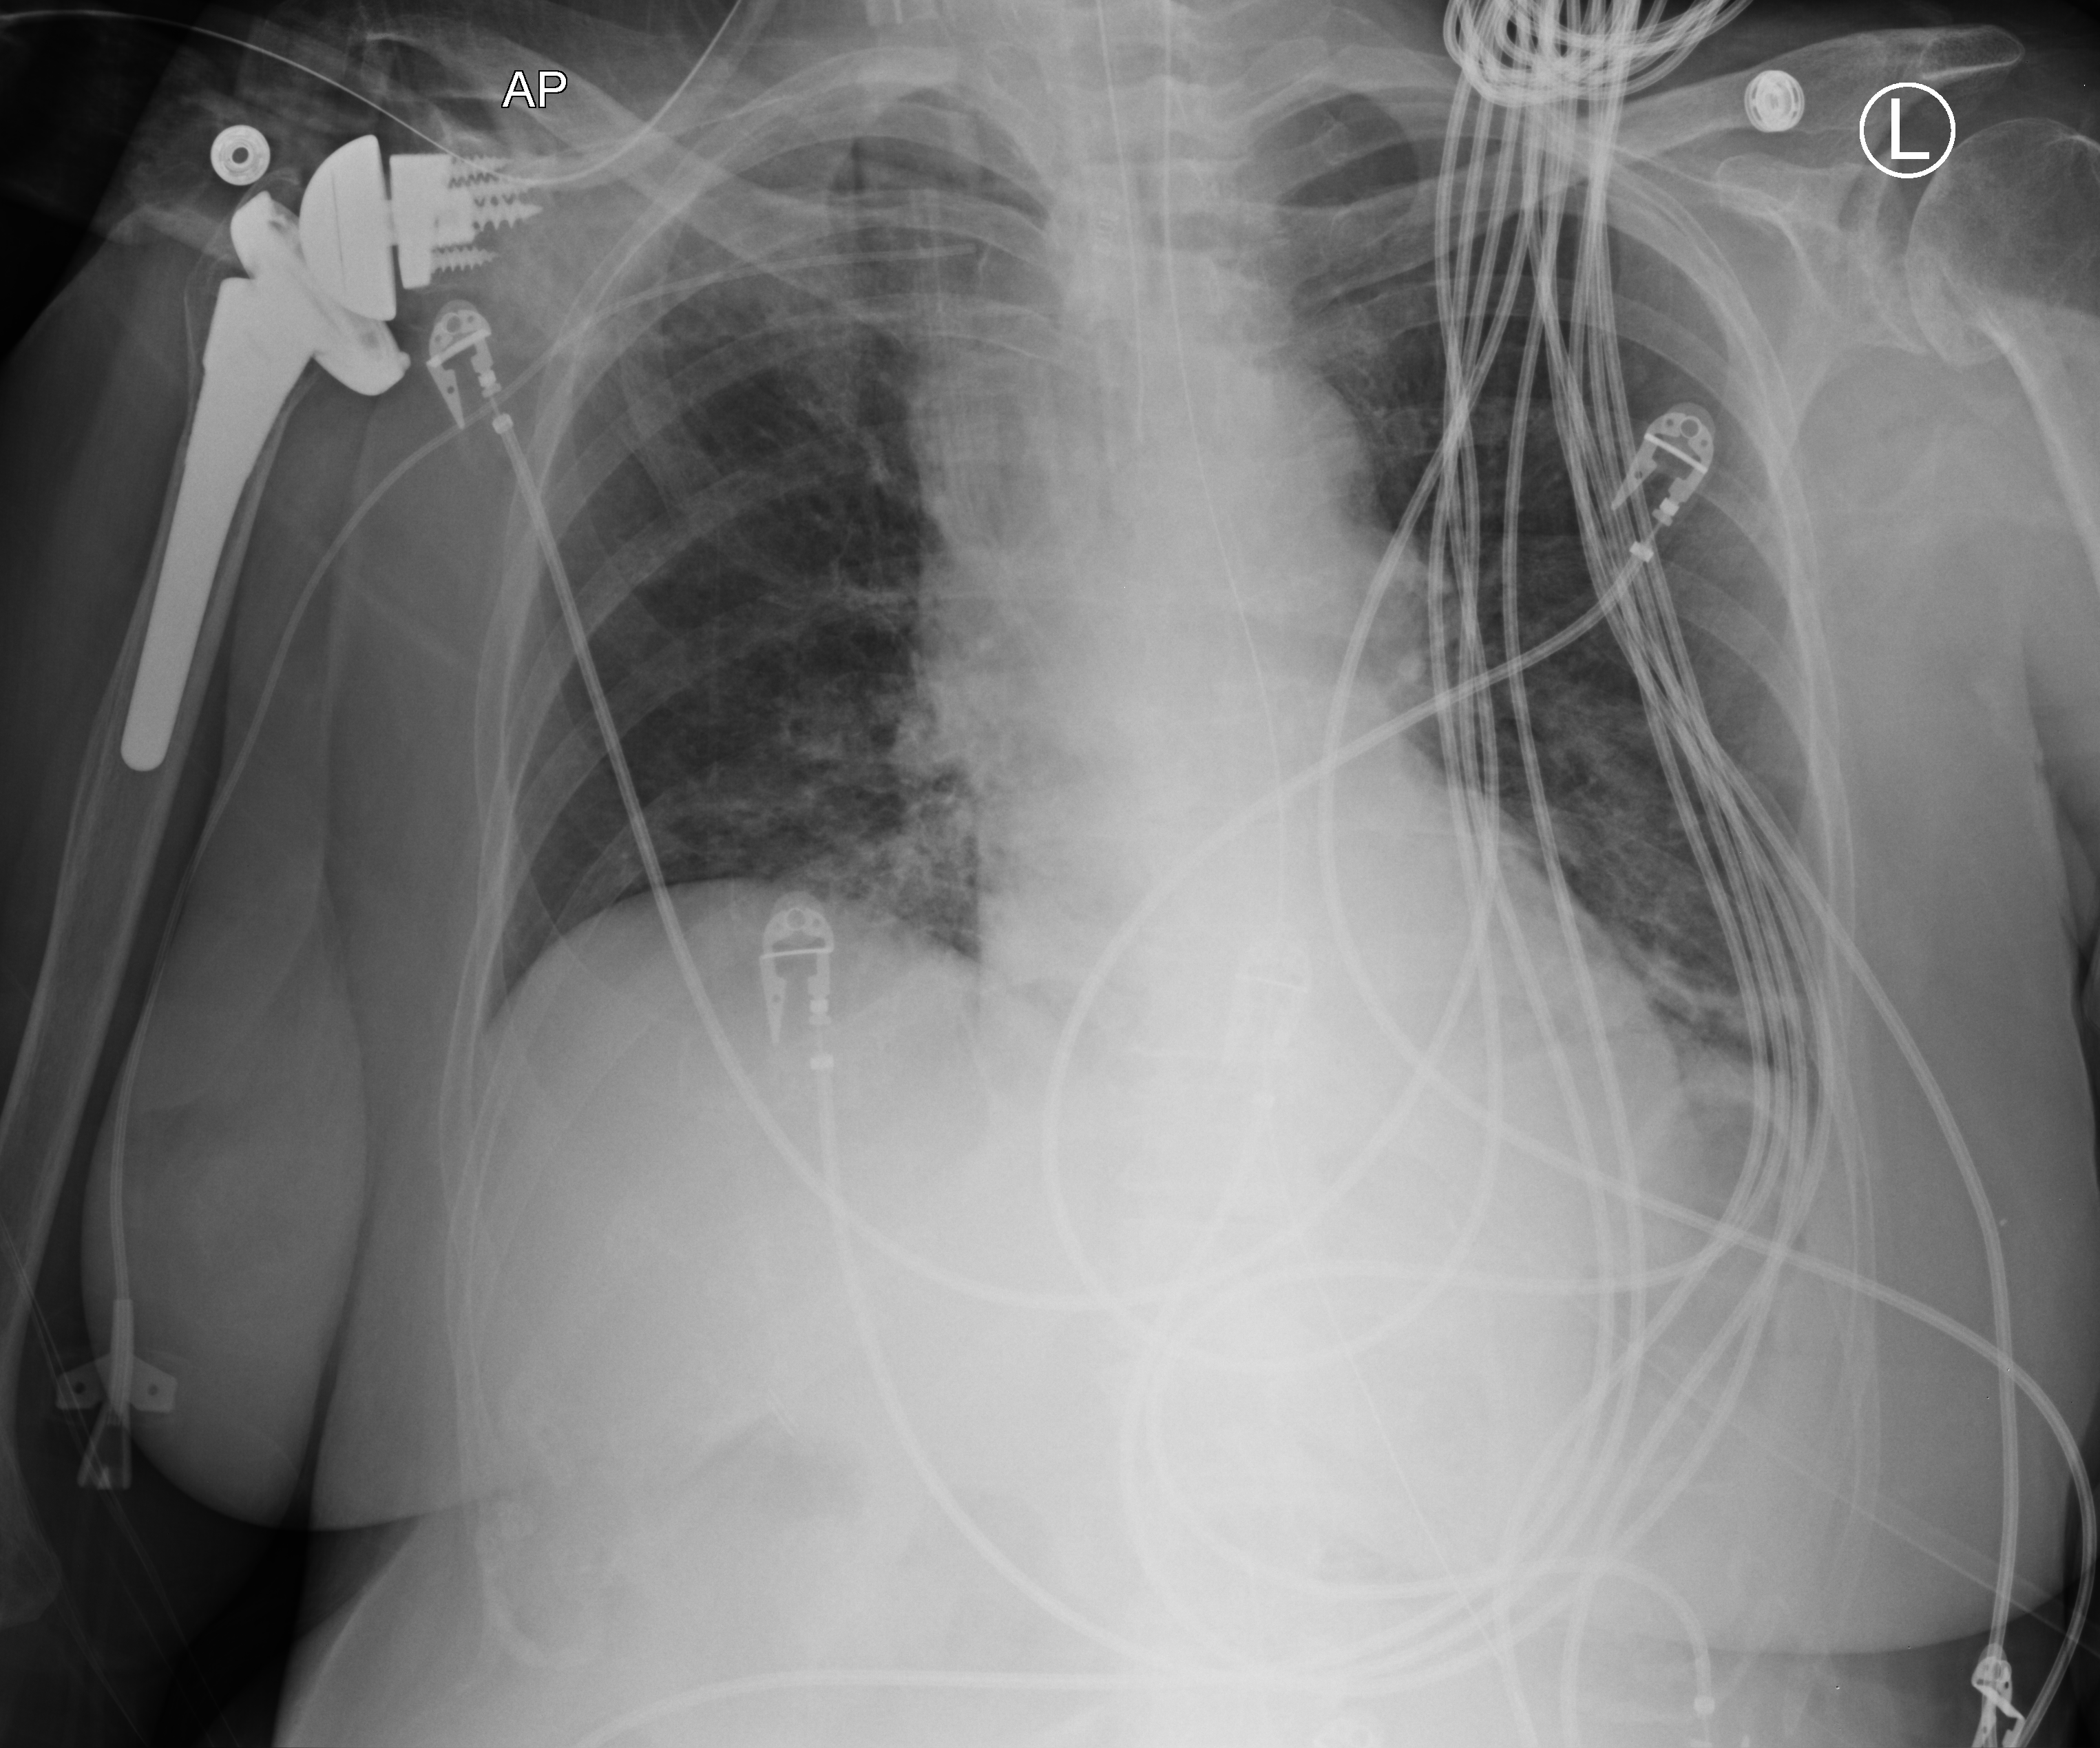
Chest X-ray (portable); anteroposterior (AP) projection. Patient hospitalised with COVID-19; female, aged 60–74 years.
Admission-level facts for this patient (not findings on this image; timing relative to this image not recorded): admitted to intensive care during this hospital stay: yes; mechanically ventilated during this hospital stay: yes; length of hospital stay: 27 days.